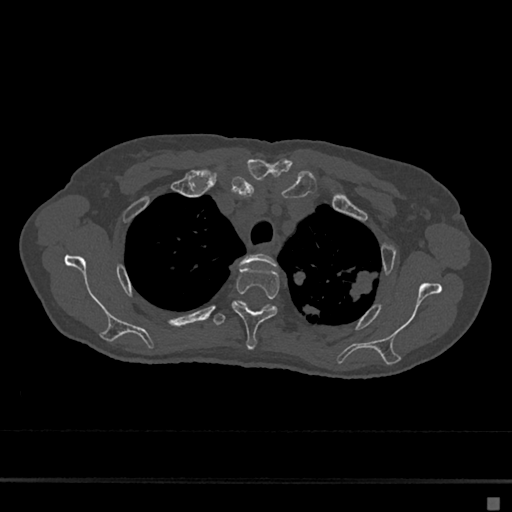
CT including the spine, one axial slice. Reconstruction kernel Br40s/3. Bone window (W 1800 / L 400 HU). 0.5 mm slice thickness. 512 × 512 image matrix, field of view 360 × 360 mm. Female patient, age 68 years. From the clinical record (not read from this slice): primary cancer: renal.
Structures marked on this image (semi-automatically segmented with operator editing):
- T2 vertebra: bounding box (x1, y1, x2, y2) in pixels: (232, 254, 277, 306)
- T3 vertebra: (232, 267, 280, 351)
- T4 vertebra: (213, 305, 273, 326)